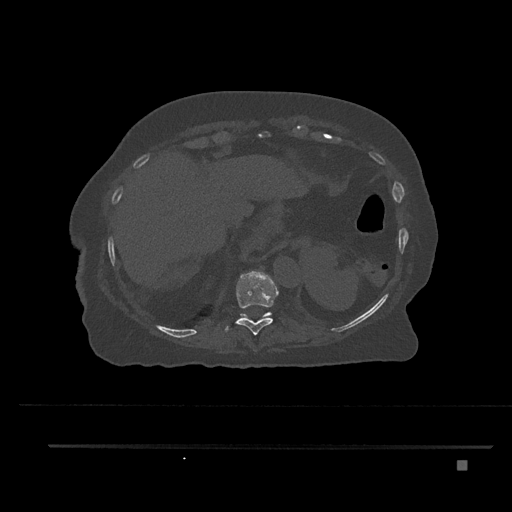
CT including the spine, one axial slice. Slice 348 of 797 in the series (ordered by position). Reconstruction kernel Br40s/3. 120 kVp. Bone window (W 1800 / L 400 HU). 0.5 mm slice thickness. 512 × 512 image matrix, field of view 437 × 437 mm. Female patient, age 76 years. Case-level facts recorded for this patient, not image findings: primary cancer: lung.
Structures marked on this image (semi-automatic segmentation, software-assisted and operator-edited):
- T10 vertebra: bounding box [x1, y1, x2, y2] px = [224, 271, 279, 335]
- T11 vertebra: [241, 312, 272, 317]